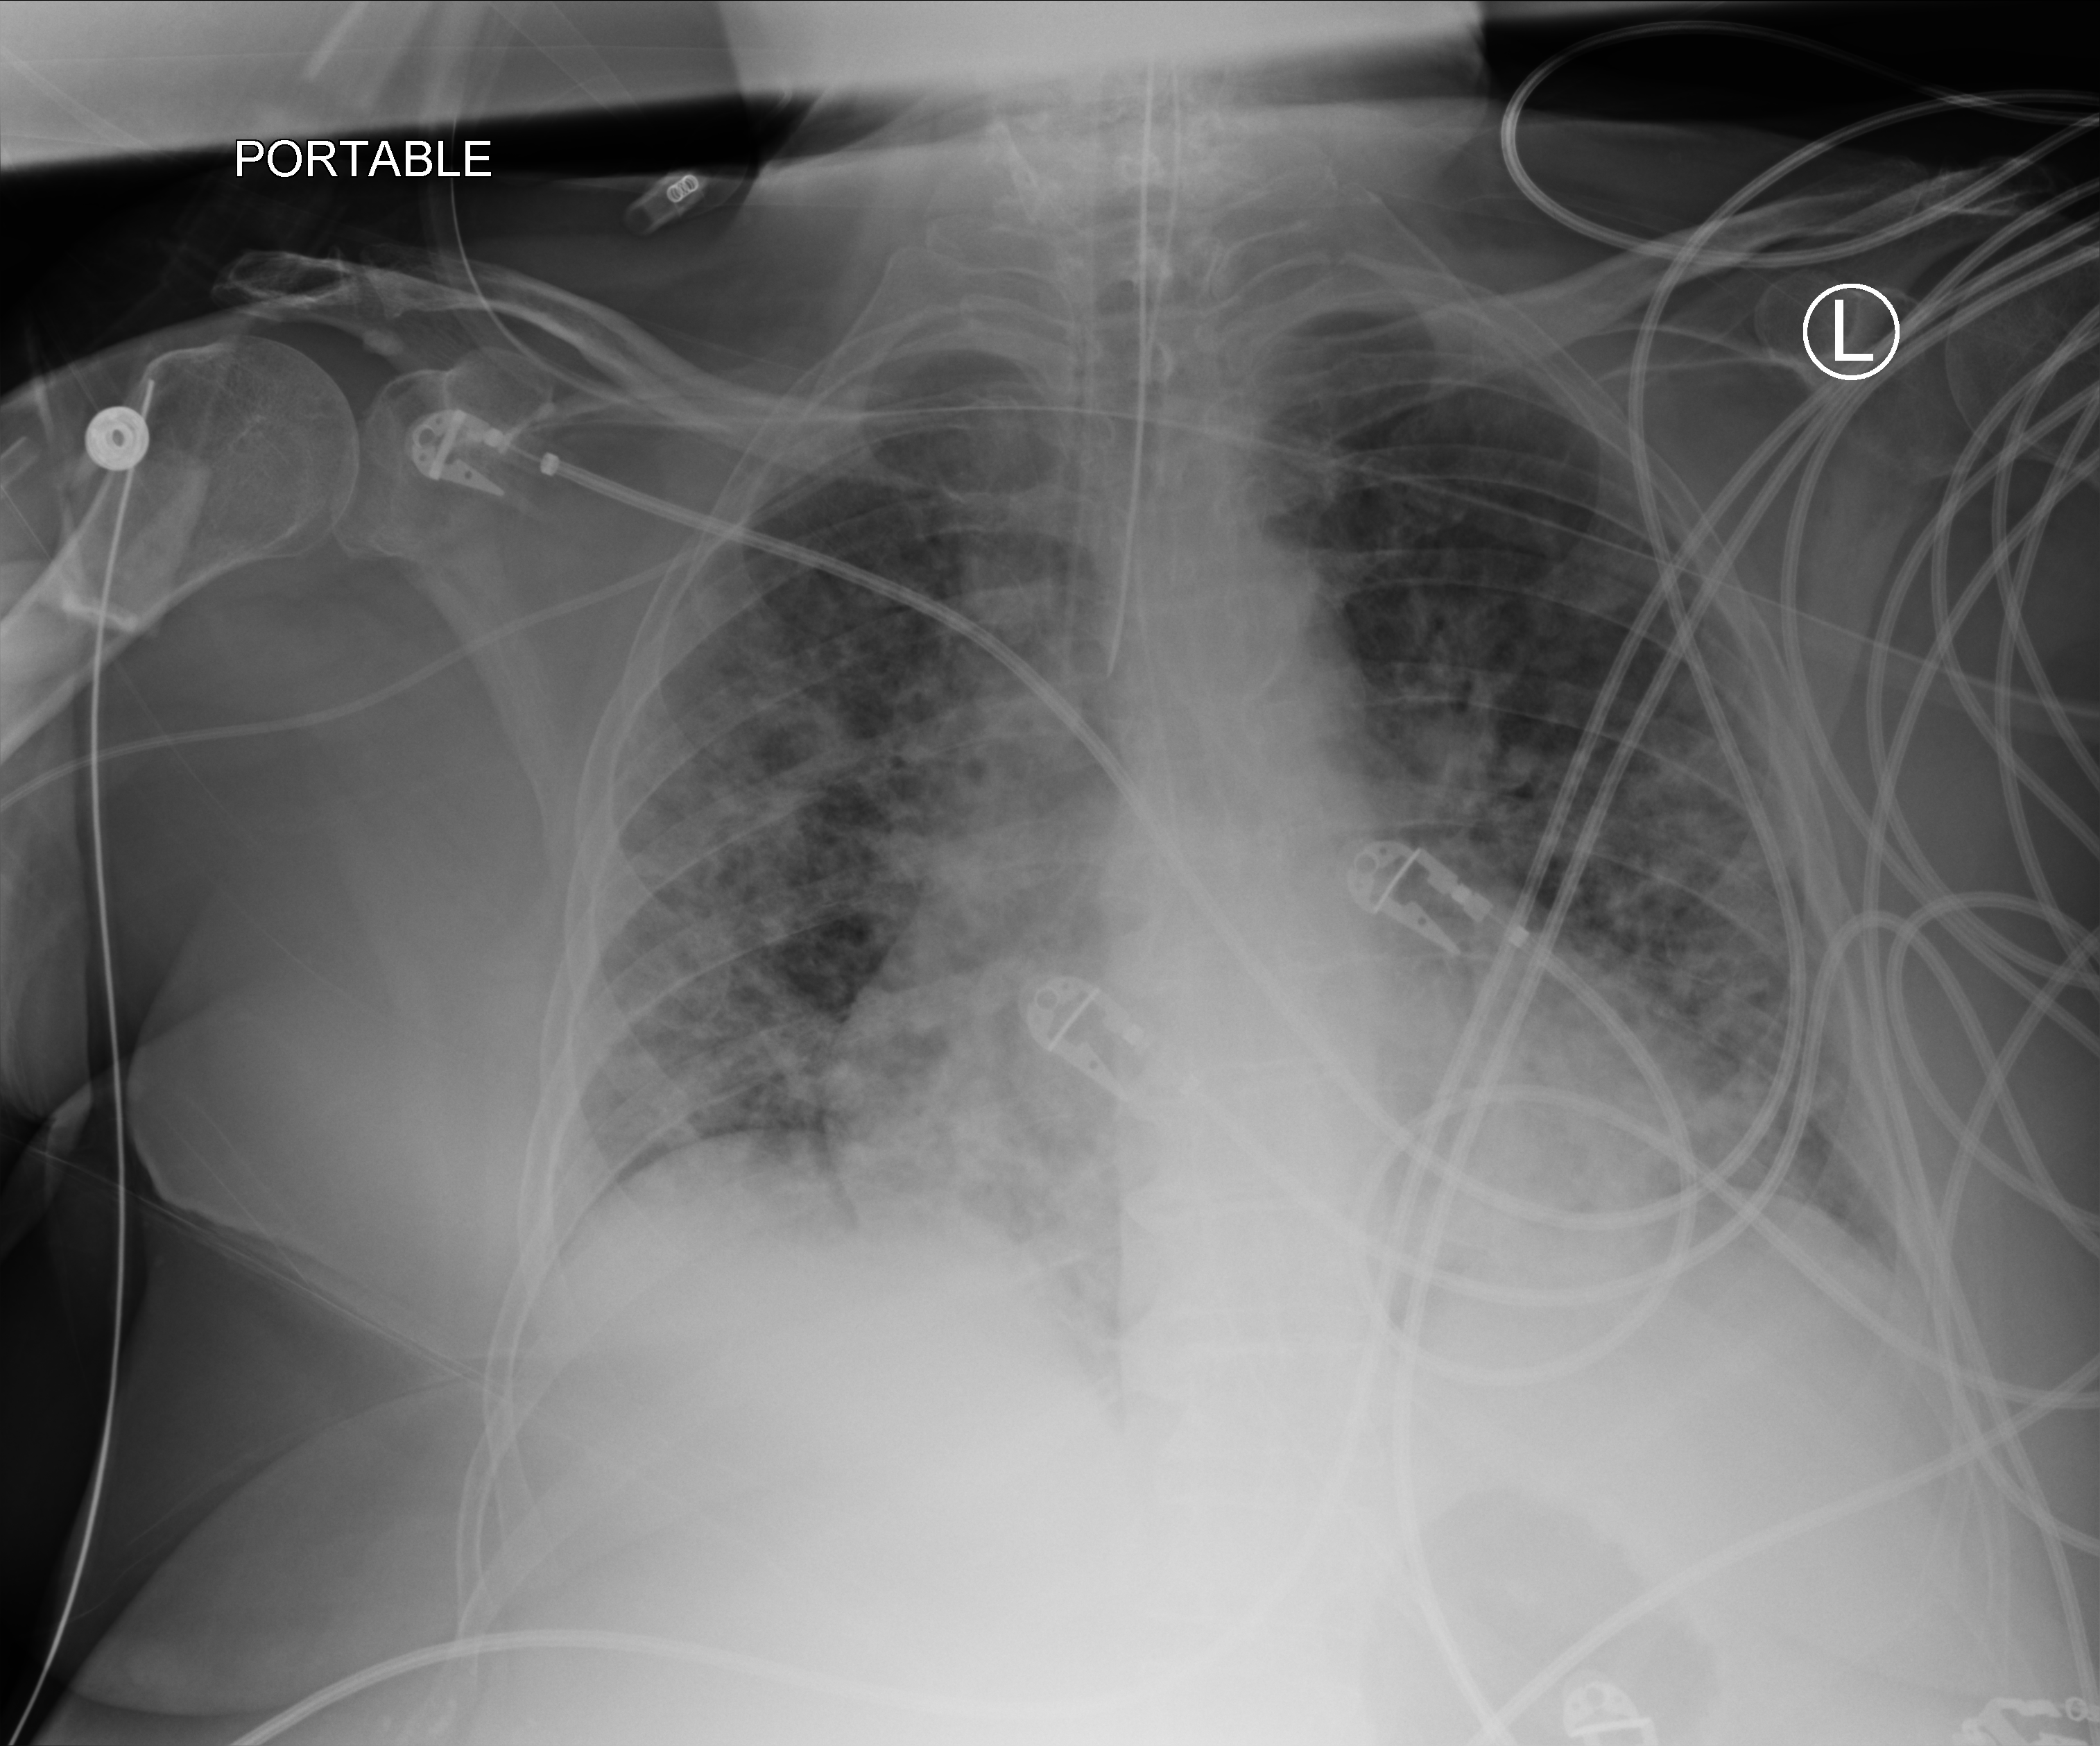
Bedside chest radiograph (computed radiography); anteroposterior (AP) projection. Female patient hospitalised with COVID-19, age 75–90 years.
Hospital-stay facts (about this admission, not read from this image; timing relative to this image not recorded):
- length of hospital stay: 31 days